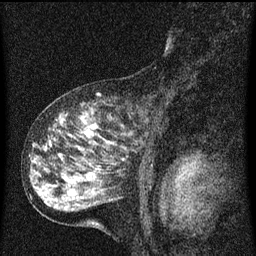
Breast MRI (dynamic contrast-enhanced), one sagittal slice; slice 33 of 60 in the series (ordered by position); dynamic contrast-enhanced series, image 2 of 3 at this slice position (ordered by acquisition); 1.5 T; TE 4.2 ms, TR 8 ms; 2 mm slice thickness; 256 × 256 image matrix. Female patient, age 55 years.
Annotated regions visible in this slice (semi-automatic segmentation, software-assisted and operator-edited):
- analysis volume of interest (the breast-tissue region the enhancement analysis was run in; not a lesion): bounding box <38,92,155,159> (left, top, right, bottom; pixels)
- tumour enhancement mask (voxels above the 70 % enhancement threshold inside the analysis volume of interest): <60,116,115,145>